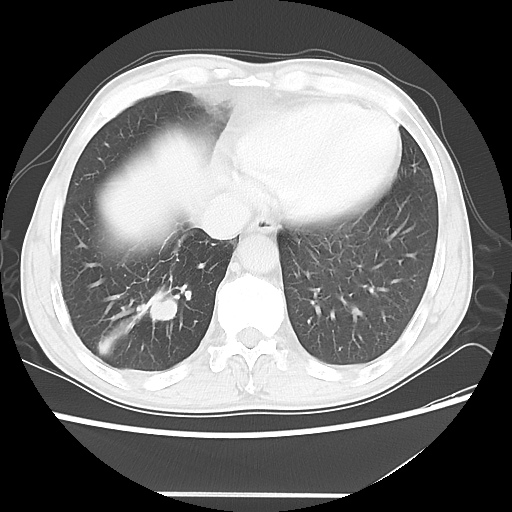
Chest CT, one axial slice; slice 13 of 56 in the series (ordered by position); reconstruction kernel LUNG; 120 kVp; lung window (W 1500 / L -600 HU); 5 mm slice thickness; 512 × 512 image matrix, field of view 344 × 344 mm. Patient: male, 65 years. From the clinical record (not read from this slice): clinical TNM (as recorded): T1c N3 M0.
Annotated regions visible in this slice (bounding box drawn by a radiologist):
- lung tumour (recorded histology: small cell carcinoma): bounding box [x1, y1, x2, y2] px = [145, 286, 189, 327]